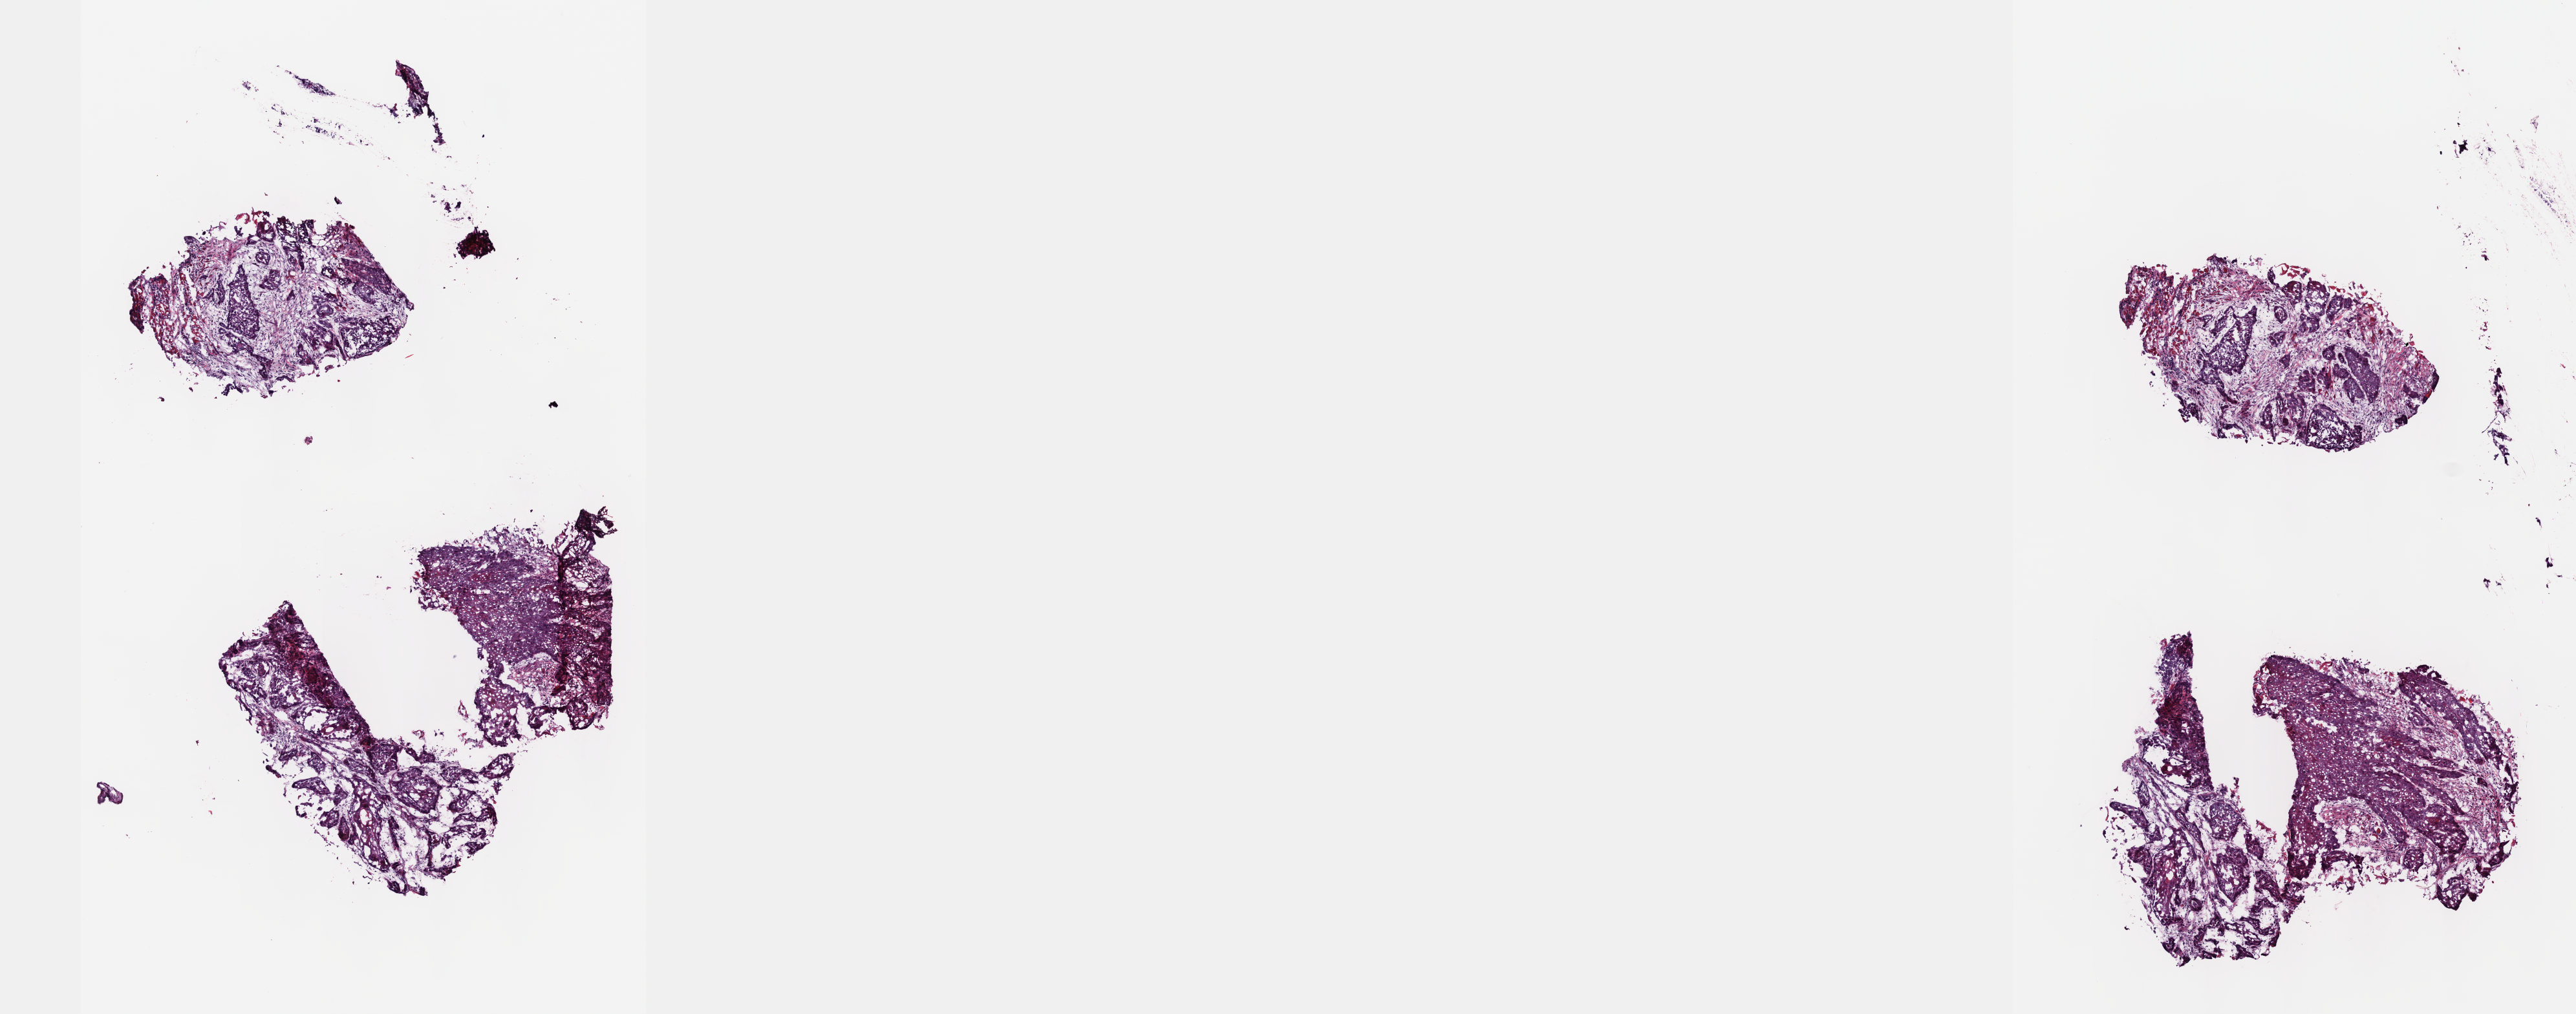
Whole-slide histology image, H&E-stained, whole scanned area (about 16.1 x 6.3 mm, from a 40x scan) shown as a low-resolution overview, frozen section, primary tumour sample from the head and neck. Male patient; age at initial diagnosis 58 years. Histologic grade: G2 (moderately differentiated). Composition of this section per pathologist review: tumour cells 80%, tumour nuclei 80%, normal cells 0%, stromal cells 20%, necrosis 0%. Inflammatory infiltration, as recorded: lymphocyte infiltration 0%, monocyte infiltration 0%, neutrophil infiltration 0%.
Diagnosis: Squamous cell carcinoma, keratinizing, NOS (floor of mouth, NOS).